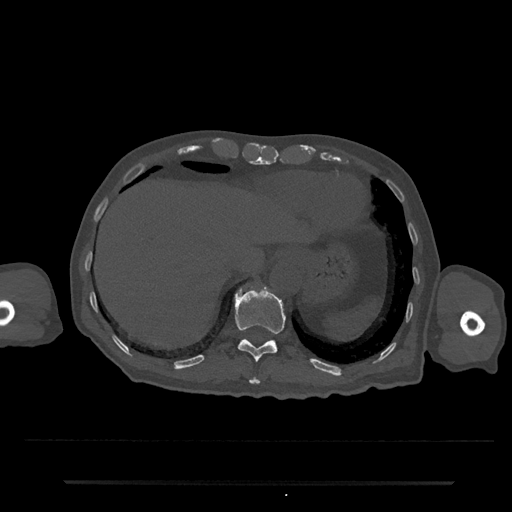
CT including the spine, one axial slice; slice 252 of 797 in the series (ordered by position); reconstruction kernel Br40s/3; bone window (W 1800 / L 400 HU); 0.5 mm slice thickness; 512 × 512 image matrix, field of view 427 × 427 mm. Patient: male, 74 years. Case-level facts recorded for this patient, not image findings: primary cancer: prostate.
Outlined on this slice (semi-automatic segmentation, software-assisted and operator-edited):
- T10 vertebra: bounding box [x1, y1, x2, y2] px = [249, 377, 260, 385]
- T11 vertebra: [234, 288, 286, 362]